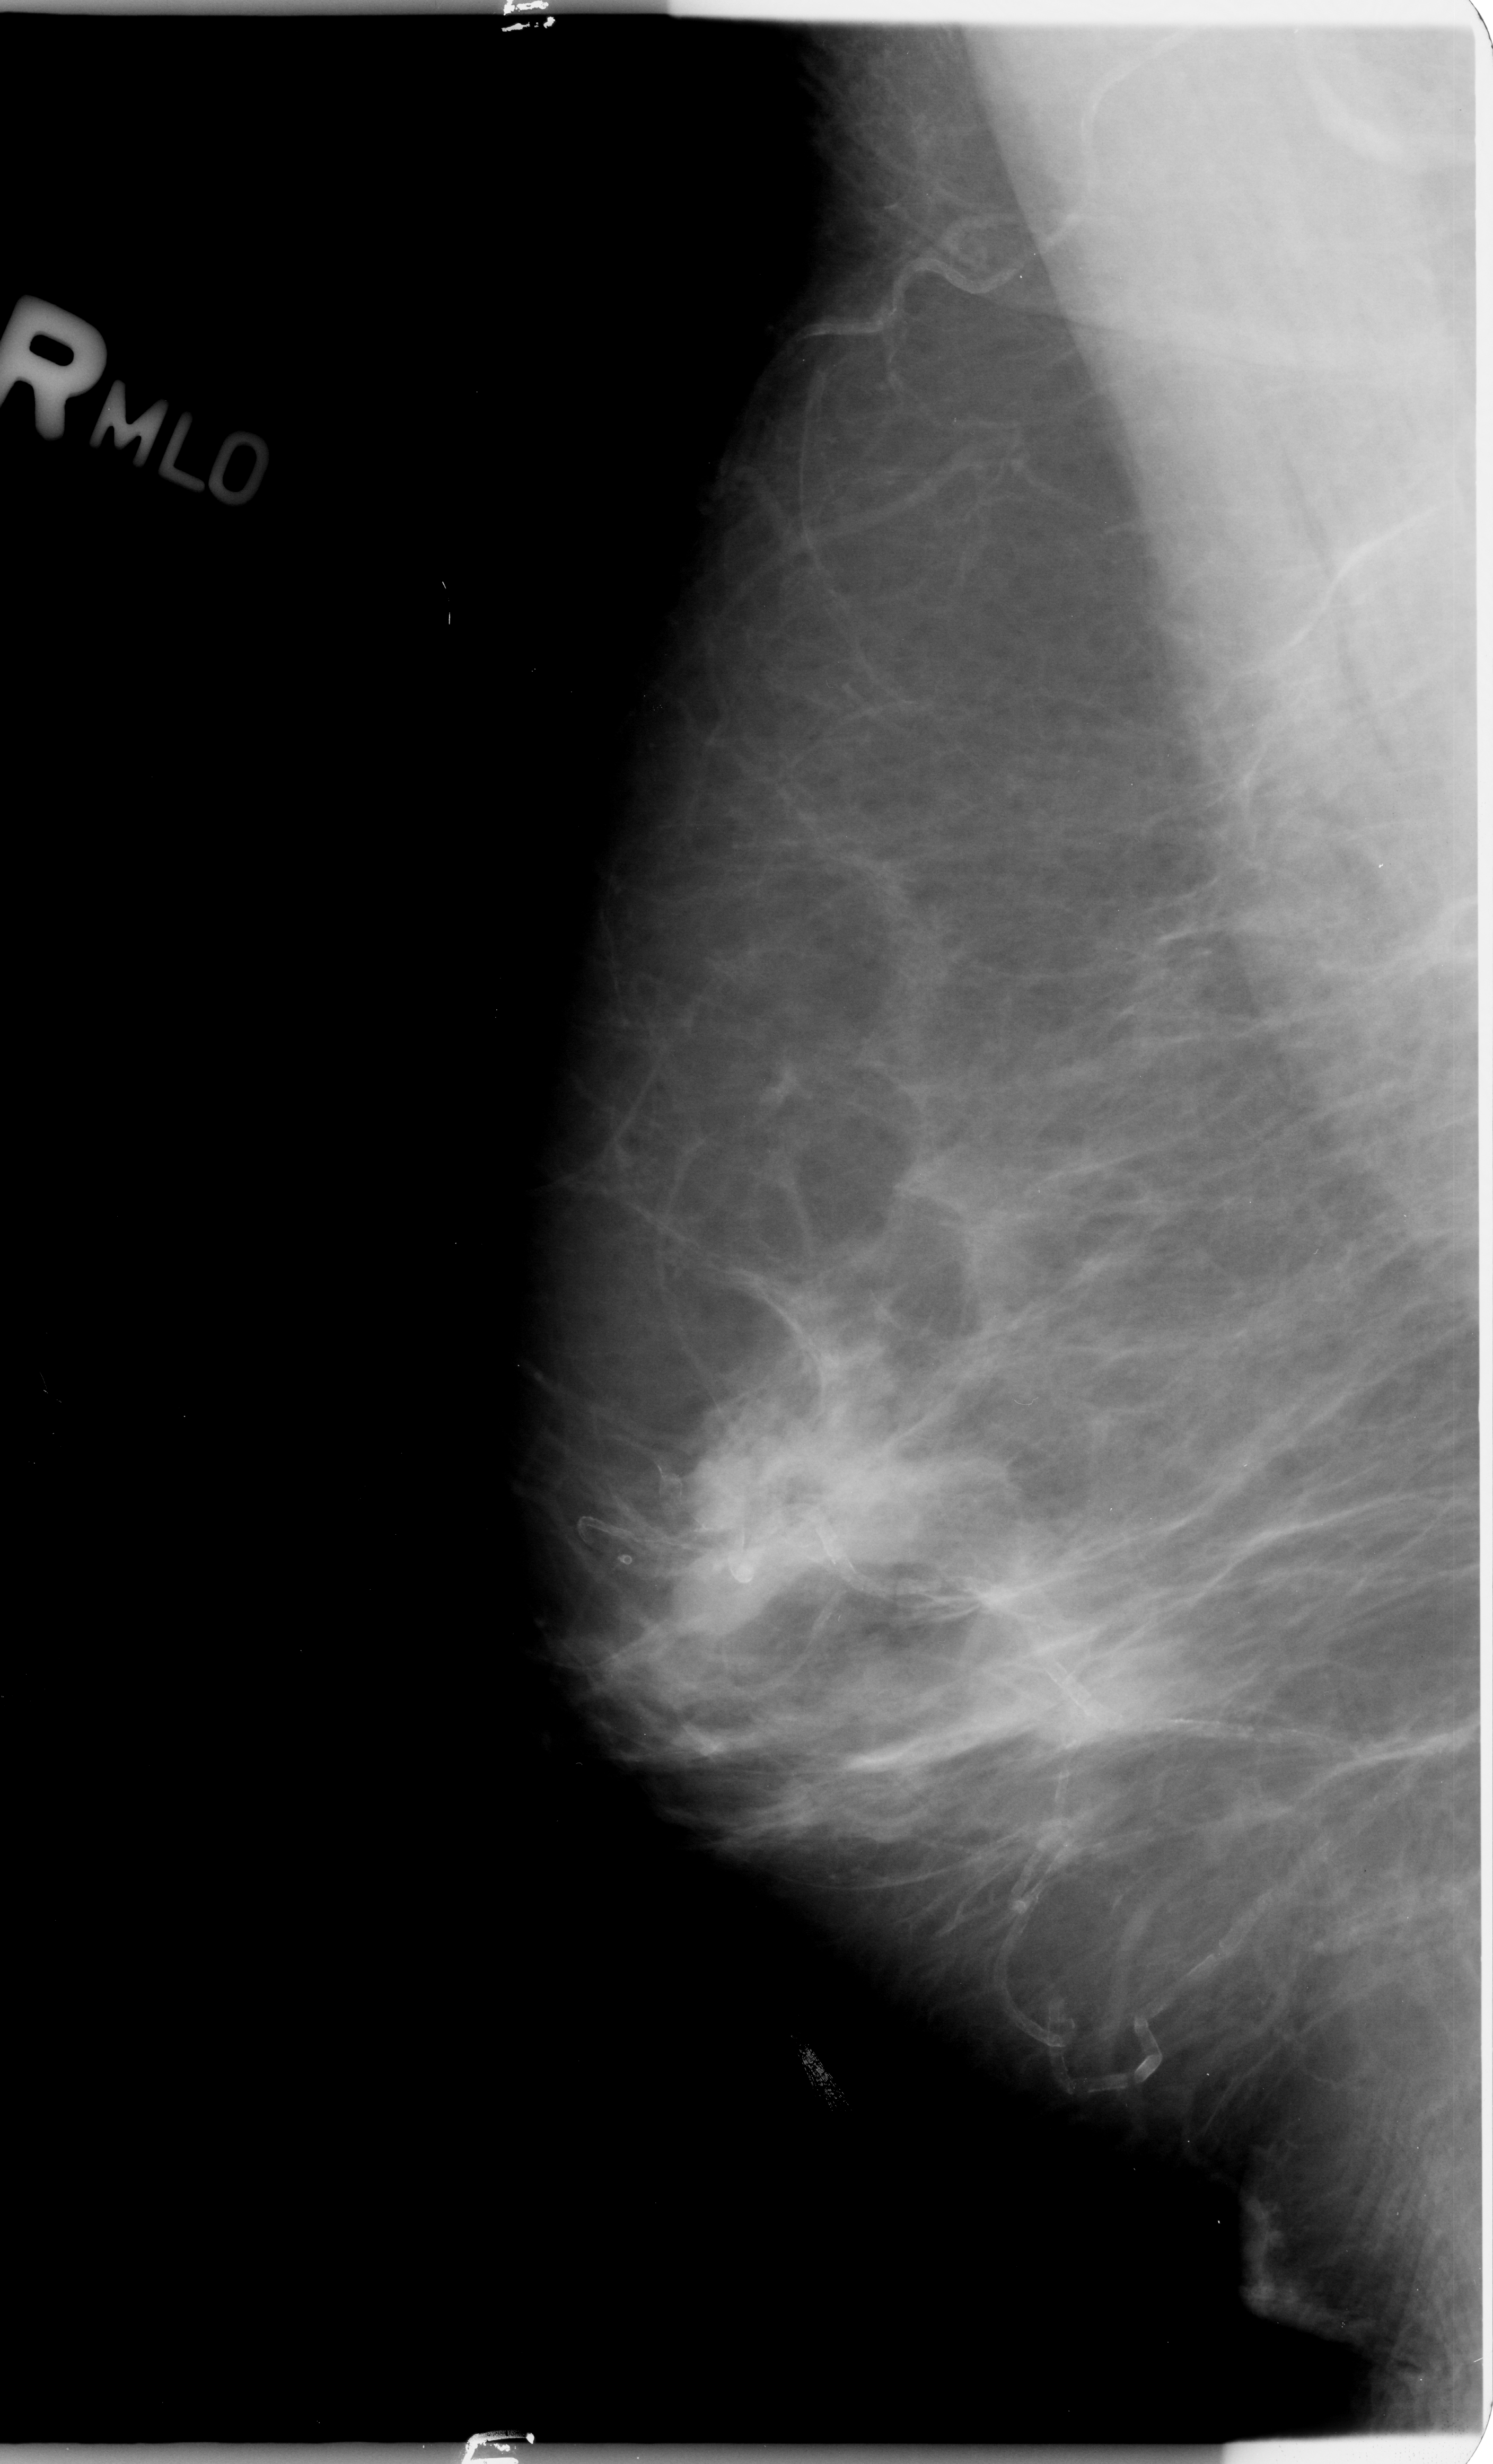
Digitized screen-film mammogram; right breast; mediolateral oblique (MLO) view; BI-RADS breast density category 3 (scale 1–4).
Abnormality record for this image: mass, shape irregular, margins obscured / ill defined; BI-RADS assessment category 3; pathology result (as recorded, not read from the image): malignant.